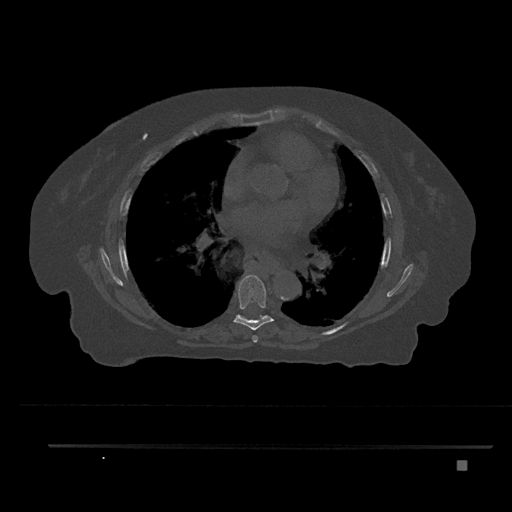
CT including the spine, one axial slice. Slice 485 of 797 in the series (ordered by position). Bone window (W 1800 / L 400 HU). 512 × 512 image matrix, field of view 437 × 437 mm. Female patient, age 76 years. From the clinical record (not read from this slice): primary cancer: lung.
Annotated regions visible in this slice (semi-automatic segmentation, software-assisted and operator-edited):
- T6 vertebra: bounding box [x1, y1, x2, y2] px = [252, 335, 258, 343]
- T7 vertebra: [234, 274, 274, 330]
- T8 vertebra: [237, 315, 269, 320]